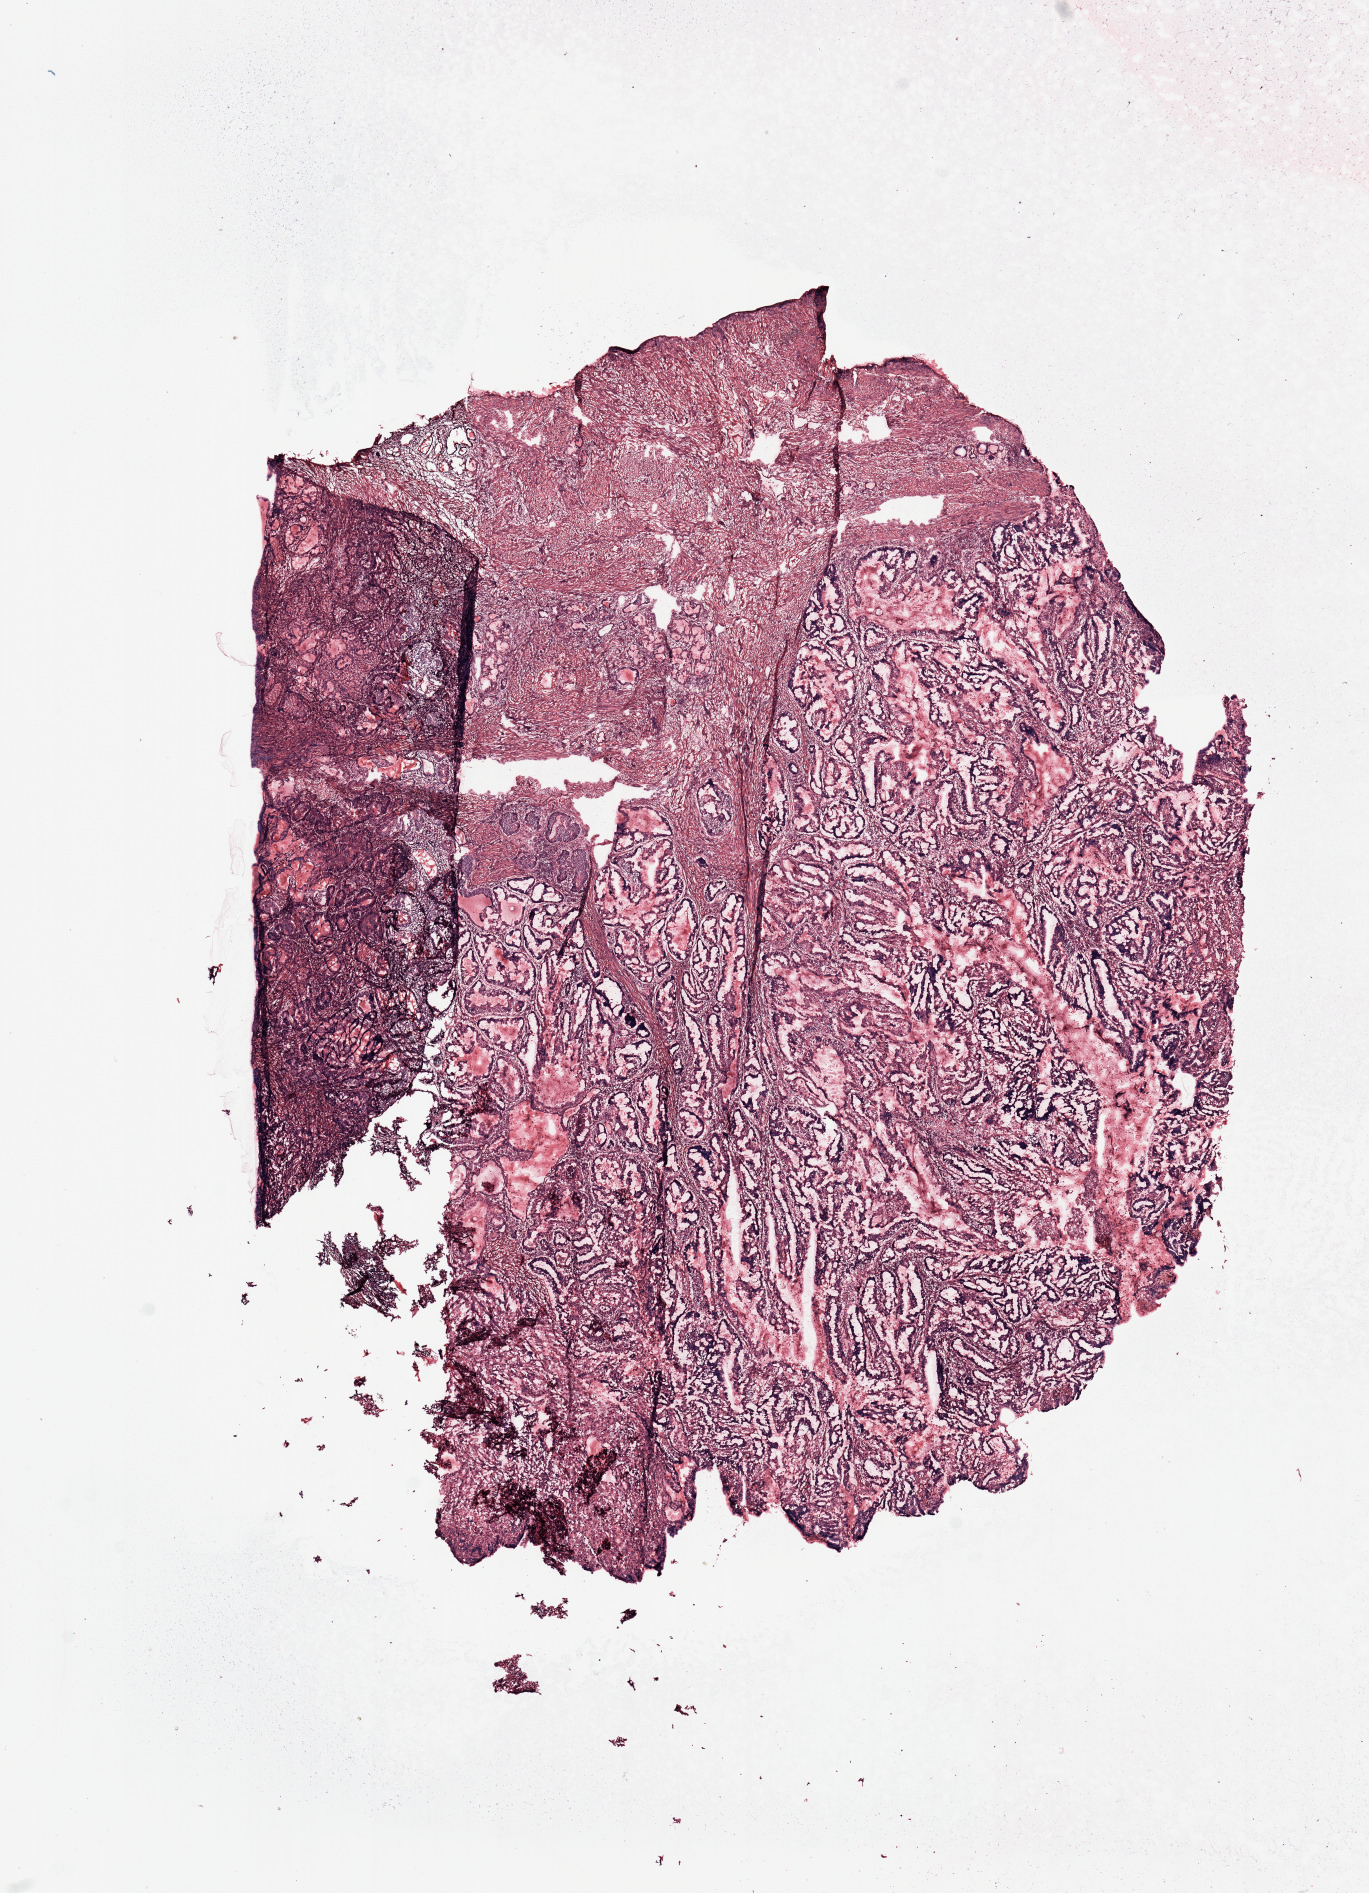
Digitized H&E-stained tissue section (whole slide), shown as a low-resolution overview of the whole scanned area (about 10.8 x 15.0 mm, slide scanned at 20x), tumour tissue sample, sampled site: uterus. 68-year-old female patient. Histologic grade: G1 (well differentiated). Pathologist review of this section (percent, as recorded): tumour nuclei 85%, necrosis 0%.
* AJCC pathologic stage: I
* diagnosis: Endometrioid adenocarcinoma, NOS